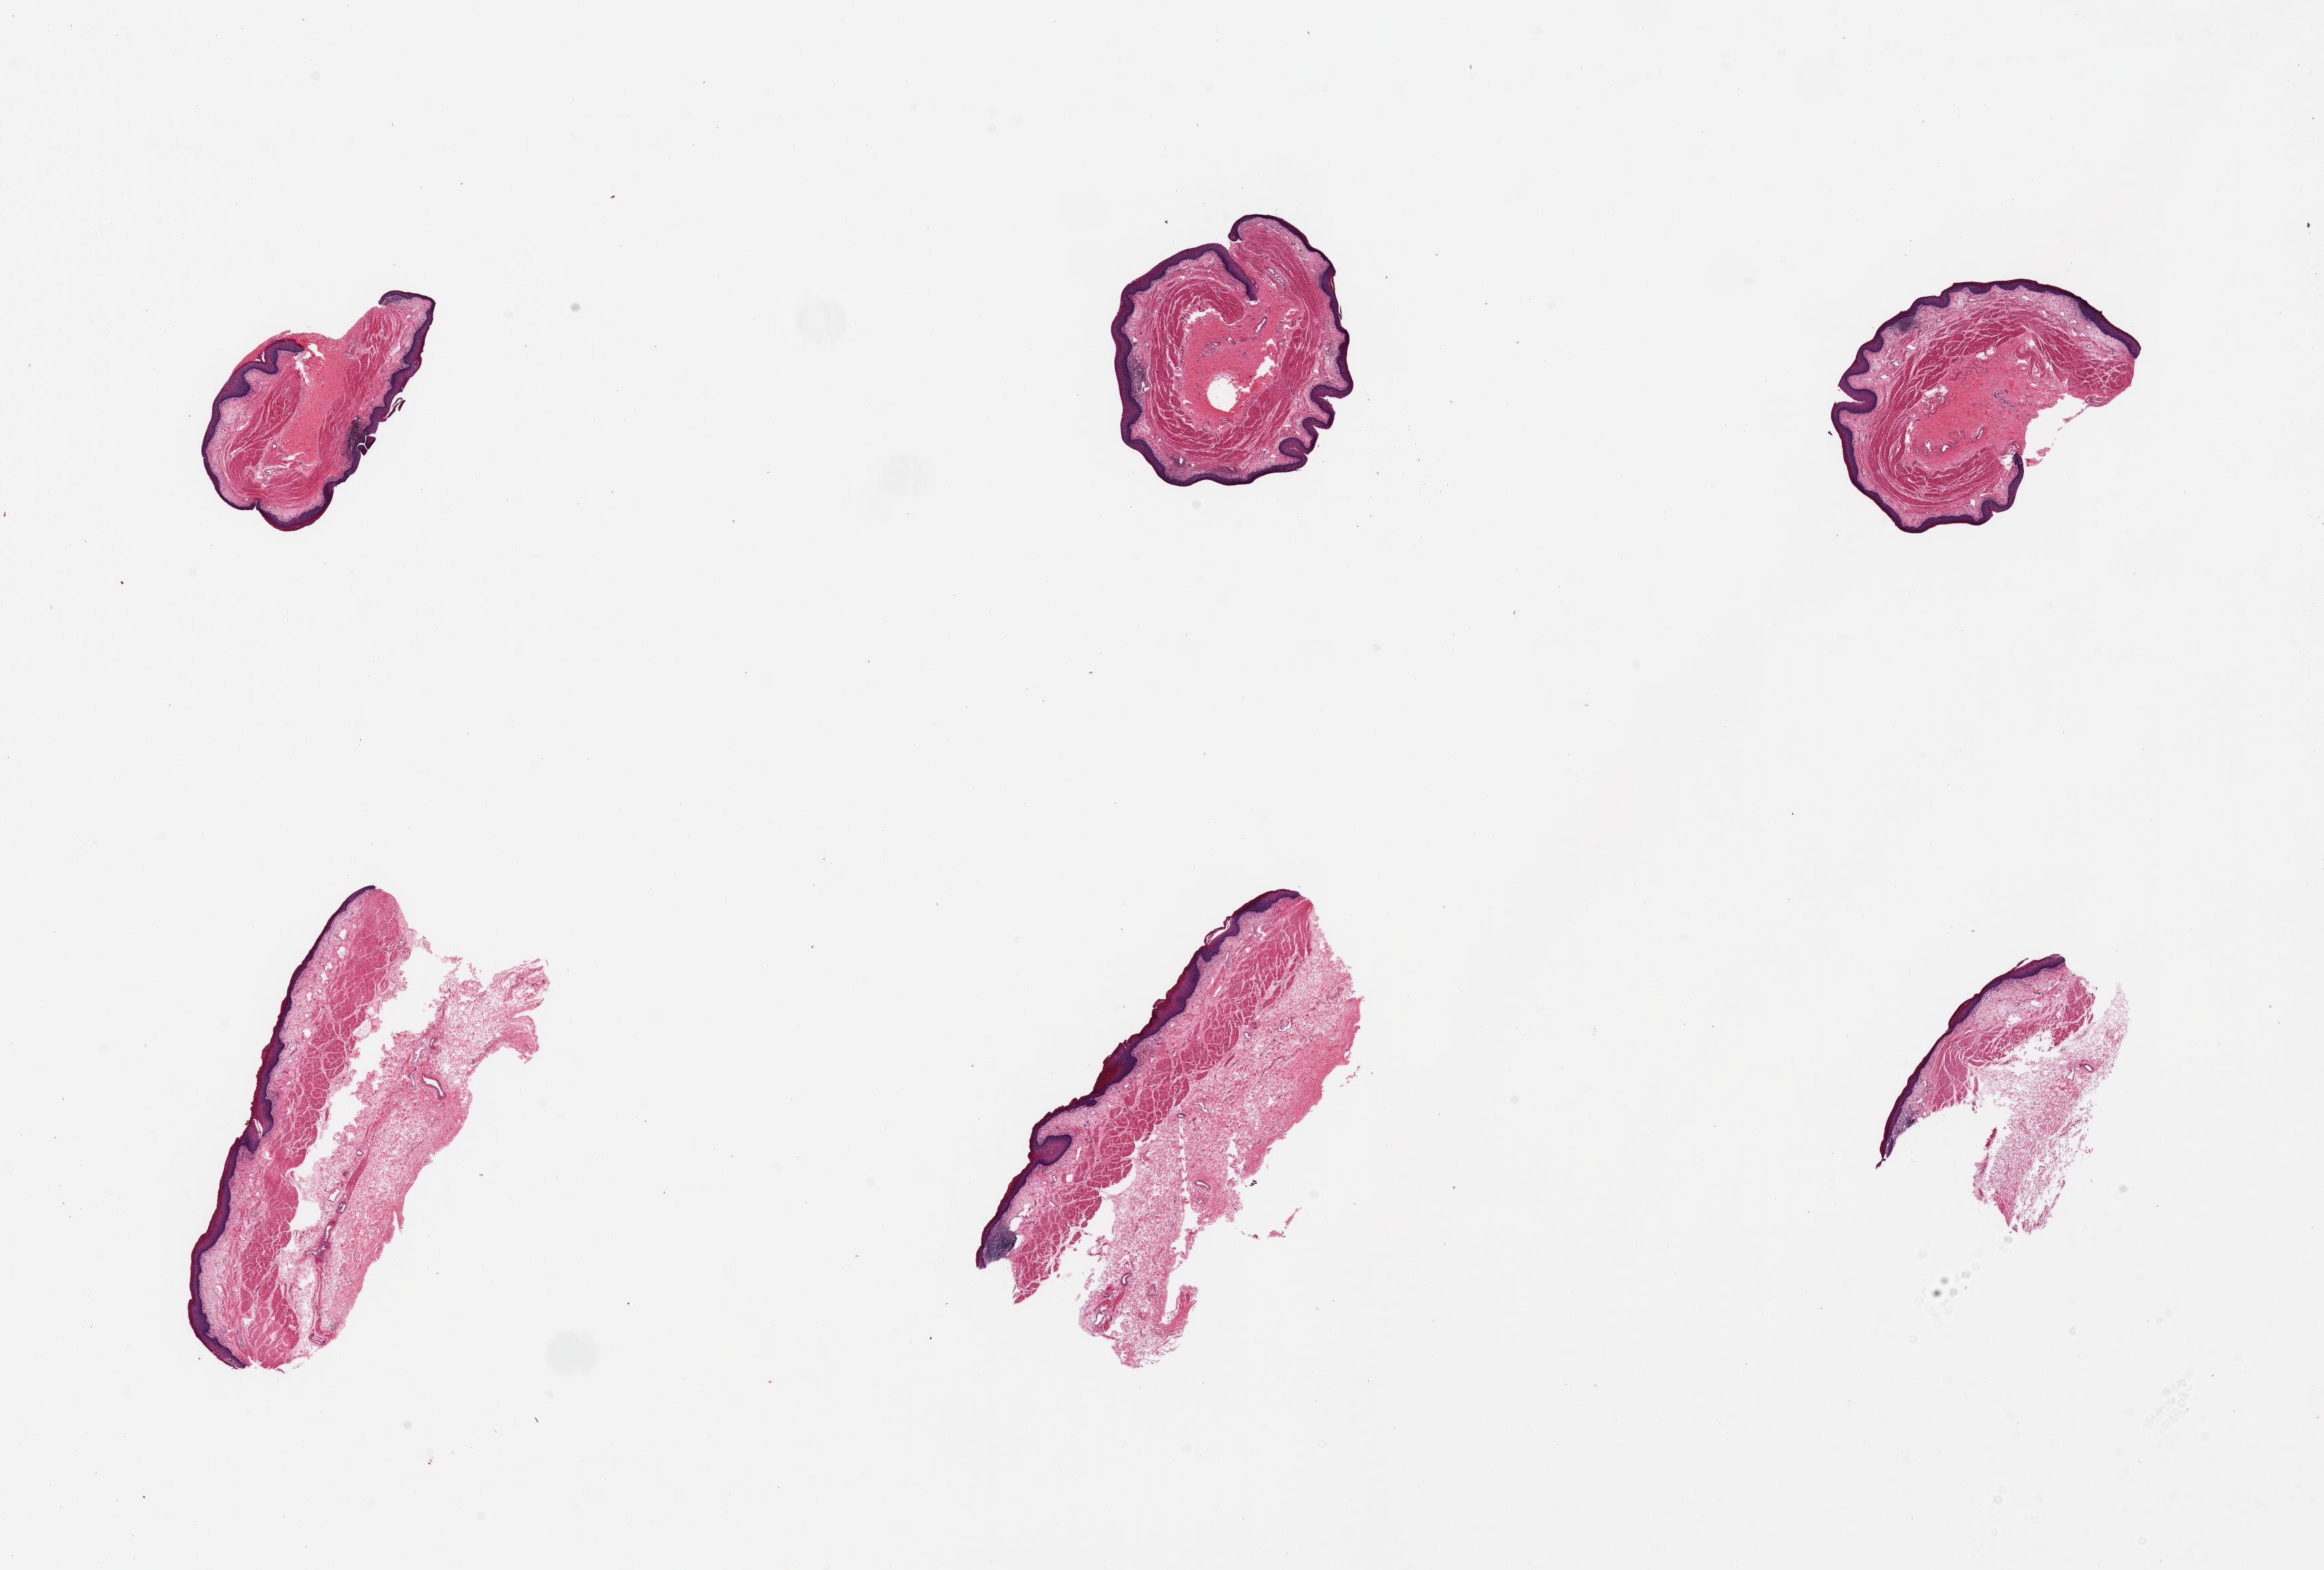
Digitized hematoxylin and eosin (H&E)-stained section, brightfield, whole scanned area (about 27.6 x 18.6 mm, slide scanned at 20x) shown as a low-resolution overview. PAXgene-fixed paraffin-embedded (PFPE) section. Section of esophageal mucous membrane (target tissue). Tissue donor sample. Donor: female.
Reviewer comment on this tissue sample: 6 pieces, up to 5.5x2.5mm; mild chronic inflammation (correlates with history of gastric reflux).